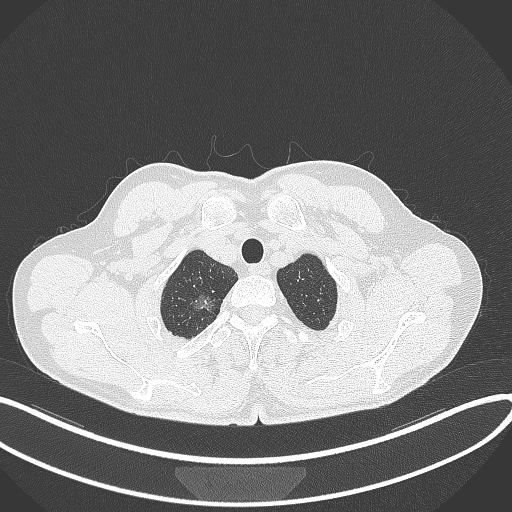
Chest CT, one axial slice. Position 350 of 407 along the scan axis. Reconstruction kernel B70f. Lung window (W 1500 / L -600 HU). 1 mm slice thickness. 512 × 512 image matrix, field of view 400 × 400 mm. Male patient, age 58 years. From the clinical record (not read from this slice): clinical TNM (as recorded): T1c N0 M0; histopathological grade: G1-2.
Structures marked on this image (rectangle marked by the reading radiologist):
- lung tumour (recorded histology: adenocarcinoma): bounding box (x1, y1, x2, y2) in pixels: (190, 290, 215, 318)